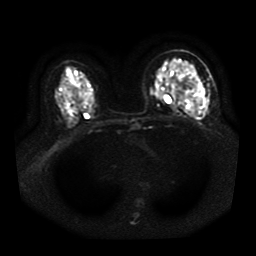
Breast MRI, one axial slice; slice 23 of 41 in the series (ordered by position); diffusion-weighted series; image 2 of 4 stored at this slice position (different b-values; order by instance number); 1.5 T; 5 mm slice thickness; 256 × 256 image matrix. Female patient.
Structures marked on this image (expert manual segmentation):
- tumour on diffusion-weighted imaging: box from (x=193, y=89) to (x=203, y=104) px